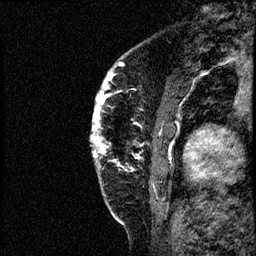
Breast MRI (dynamic contrast-enhanced), one sagittal slice. Position 12 of 60 along the scan axis. Dynamic contrast-enhanced study with each time point stored as its own series, time point 2 of 4 at this slice position (early post-contrast, ordered by acquisition time). 1.5 T. TE 4.2 ms, TR 17.6 ms. 2 mm slice thickness. 256 × 256 image matrix, field of view 200 × 200 mm. Patient: female, 40 years. From the clinical record (not read from this slice): setting: breast cancer imaged before/during neoadjuvant chemotherapy; receptor status: HER2-positive.
Structures marked on this image (semi-automatic segmentation, software-assisted and operator-edited):
- analysis volume of interest (the breast-tissue region the enhancement analysis was run in; not a lesion): bounding box <91,56,197,205> (left, top, right, bottom; pixels)
- tumour enhancement mask (voxels above the 100 % enhancement threshold inside the analysis volume of interest): <91,62,160,169>